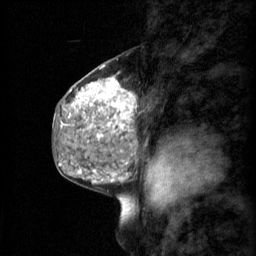
Breast MRI (dynamic contrast-enhanced), one sagittal slice. Position 32 of 60 along the scan axis. 3 images stored at this slice position (order not interpretable as contrast timing). 1.5 T. TE 4.2 ms, TR 11 ms. 256 × 256 image matrix, field of view 200 × 200 mm. Patient: female, 48 years.
Outlined on this slice (semi-automatic segmentation, software-assisted and operator-edited):
- analysis volume of interest (the breast-tissue region the enhancement analysis was run in; not a lesion): box from (x=69, y=74) to (x=143, y=147) px
- tumour enhancement mask (voxels above the 70 % enhancement threshold inside the analysis volume of interest): (x=77, y=78)–(x=137, y=147)